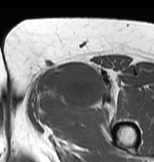
MRI of an extremity soft-tissue mass, one axial slice; position 41 of 83 along the scan axis; MR volume resampled by the dataset authors to the PET/CT grid (not the native acquisition matrix); 3.27 mm slice thickness; 154 × 162 image matrix. Female patient. Case-level facts recorded for this patient, not image findings: histological type: myxofibrosarcoma; grade: intermediate; site of the primary tumour: left thigh.
Annotated regions visible in this slice (expert contour drawn on MRI and transferred to this co-registered scan by the dataset authors):
- gross tumour volume including surrounding oedema: box from (x=26, y=64) to (x=120, y=119) px
- gross tumour volume (mass): (x=39, y=64)–(x=102, y=106)